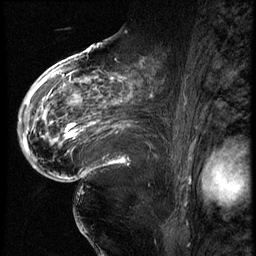
Breast MRI (dynamic contrast-enhanced), one sagittal slice; position 38 of 62 along the scan axis; 3 images stored at this slice position (order not interpretable as contrast timing); 1.5 T; TE 4.2 ms, TR 9 ms; 2.5 mm slice thickness; 256 × 256 image matrix. Patient: female, 56 years. From the clinical record (not read from this slice): setting: breast cancer imaged before/during neoadjuvant chemotherapy; receptor status: HER2-positive.
Structures marked on this image (semi-automatically segmented with operator editing):
- analysis volume of interest (the breast-tissue region the enhancement analysis was run in; not a lesion): bounding box <84,75,181,153> (left, top, right, bottom; pixels)
- tumour enhancement mask (voxels above the 140 % enhancement threshold inside the analysis volume of interest): <84,77,152,101>